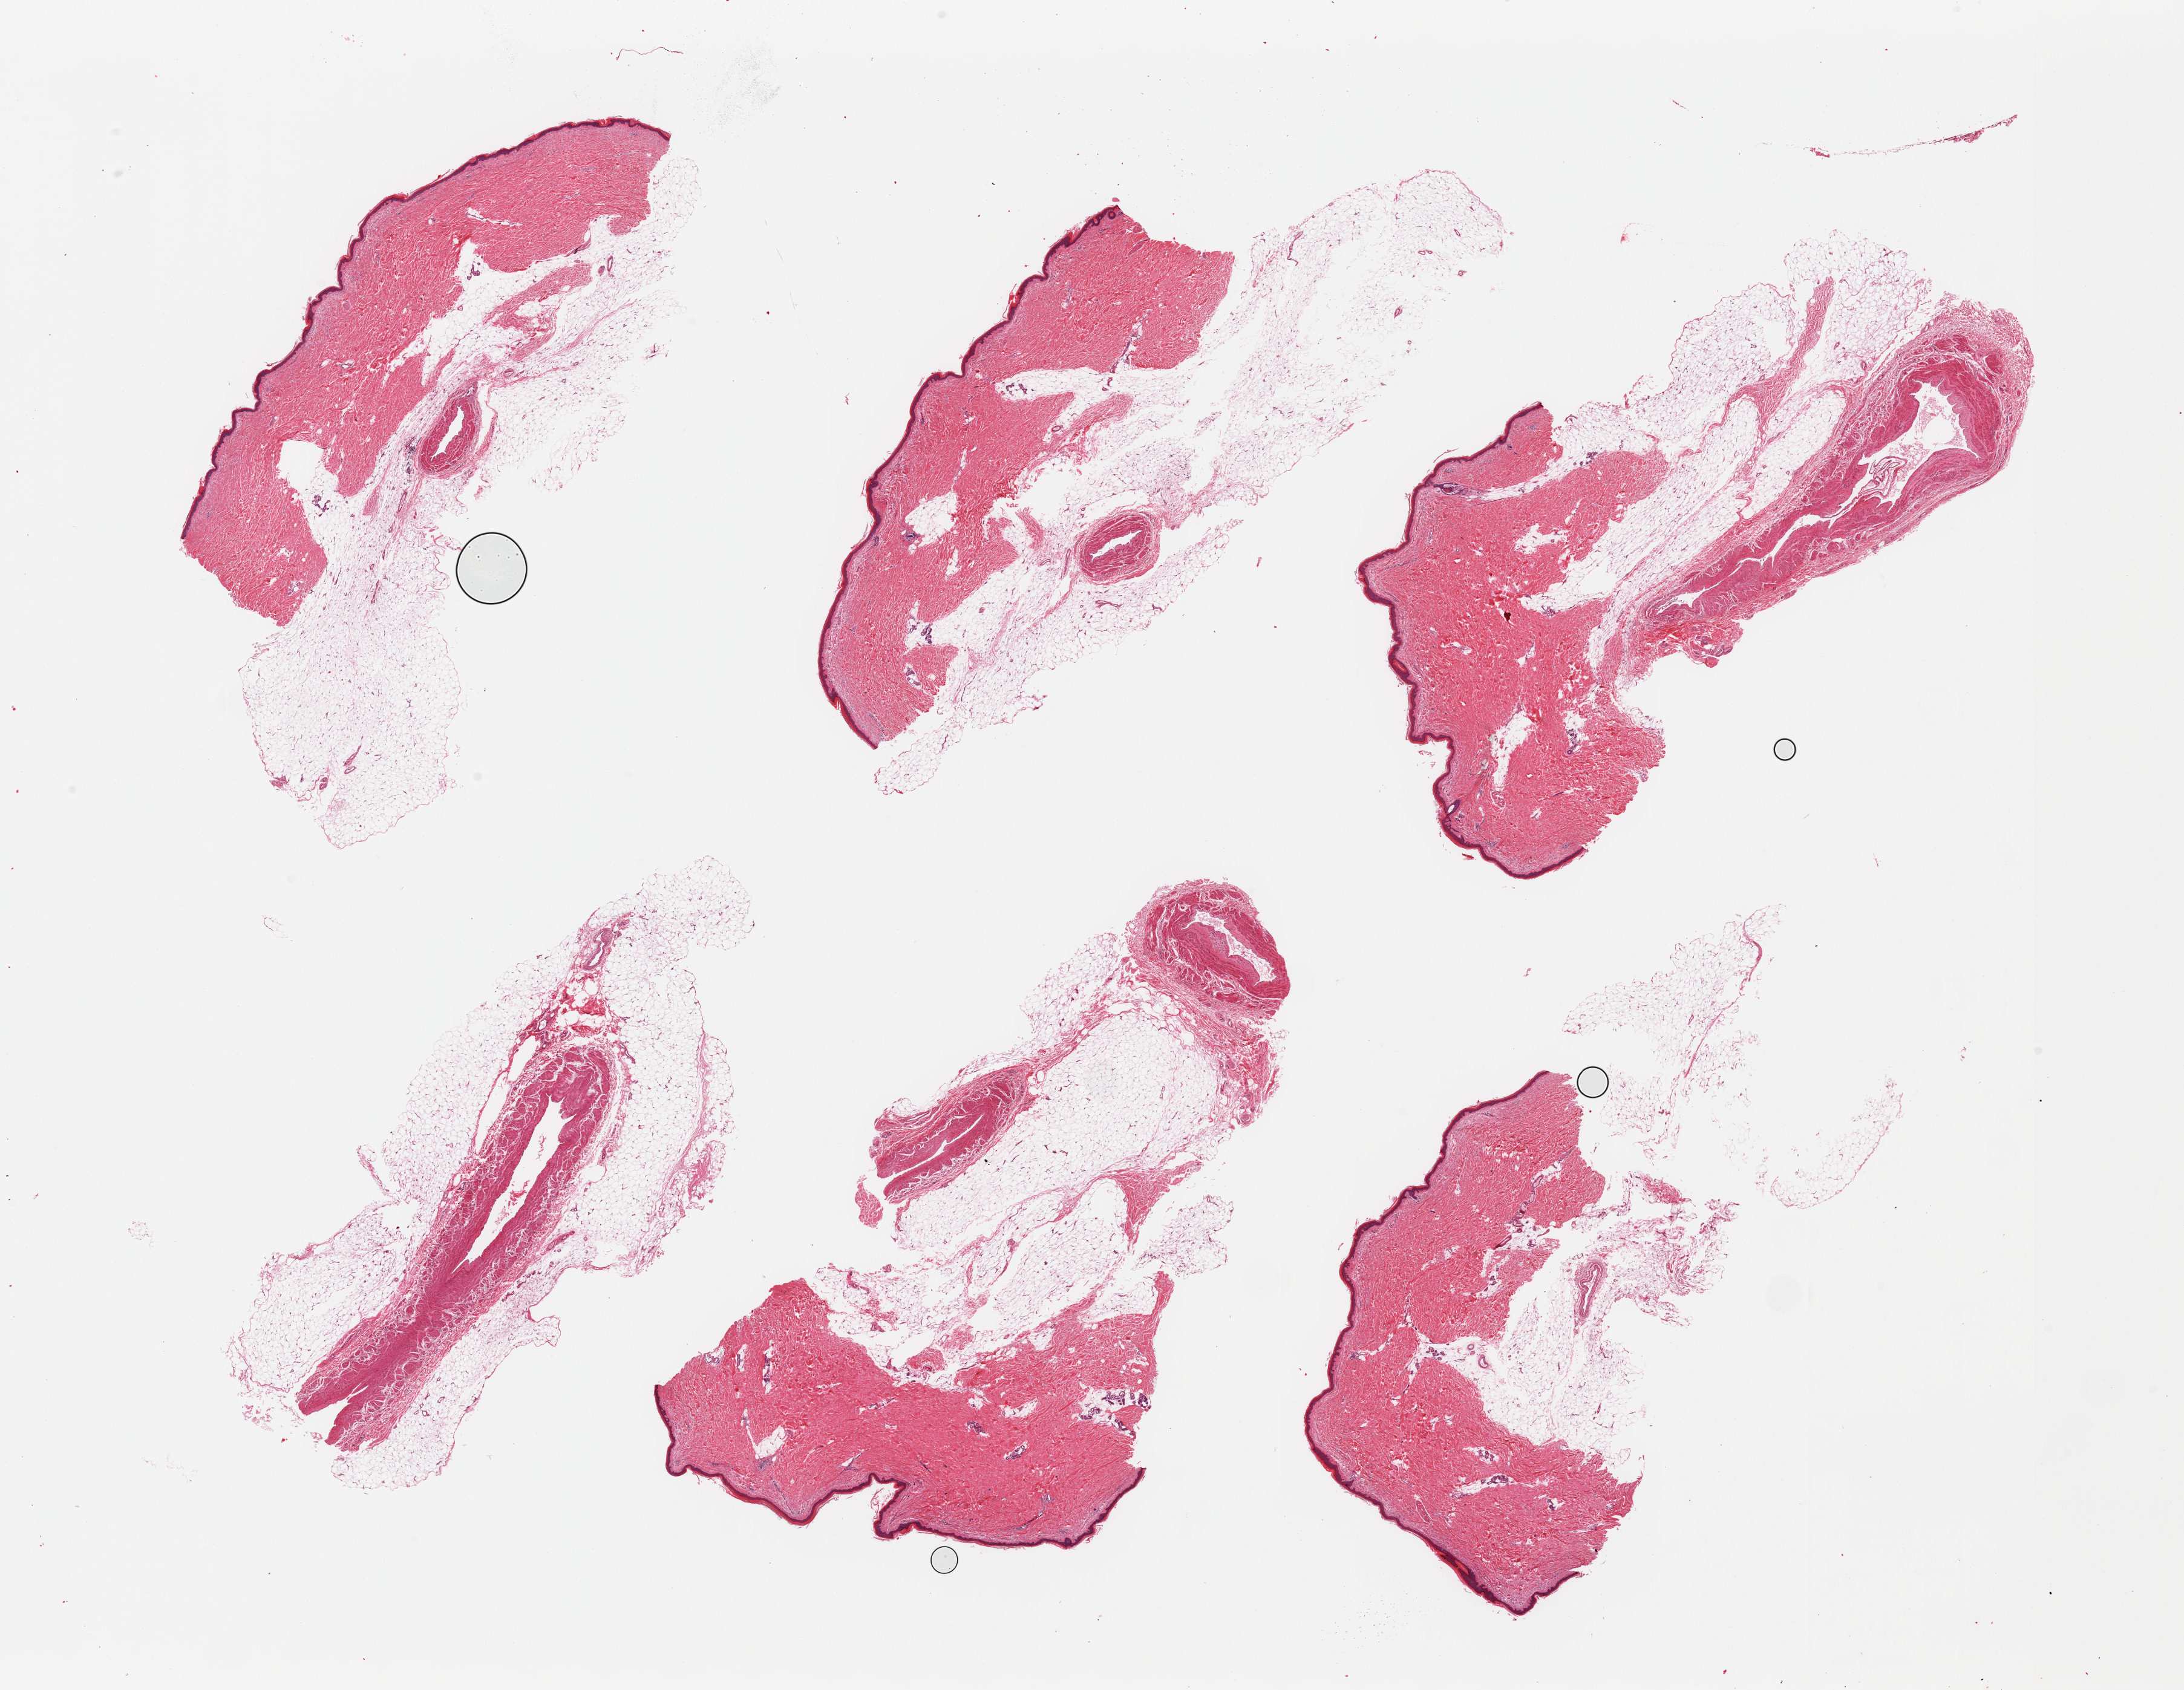
Haematoxylin and eosin whole-slide image, brightfield — shown as a low-resolution overview of the whole scanned area (about 28.5 x 22.1 mm, slide scanned at 20x). PAXgene-fixed, paraffin-embedded tissue. Sampled site (target tissue): skin of lower leg. Donor tissue sample.
Pathologist's review note for this sample: 6 pieces; includes up to ~50% mostly attached fat and large vessels, epidermis measures about 34 microns, one piece is only fat and vessel.